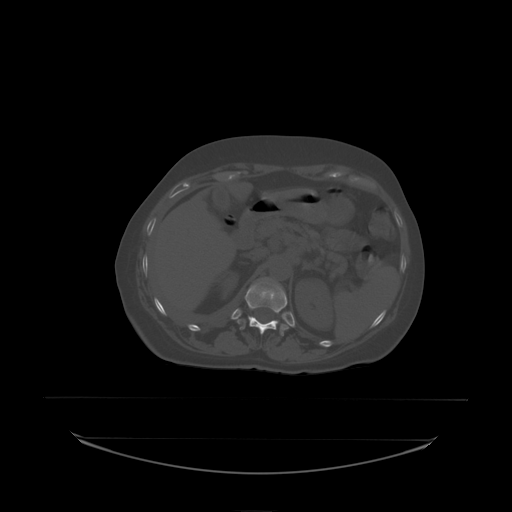
CT including the spine, one axial slice. Position 93 of 242 along the scan axis. Bone window (W 1800 / L 400 HU). 2.5 mm slice thickness. 512 × 512 image matrix, field of view 500 × 500 mm. Patient: female, 53 years. From the clinical record (not read from this slice): primary cancer: lung.
Annotated regions visible in this slice (semi-automatic segmentation, software-assisted and operator-edited):
- T12 vertebra: bounding box <238,282,289,334> (left, top, right, bottom; pixels)